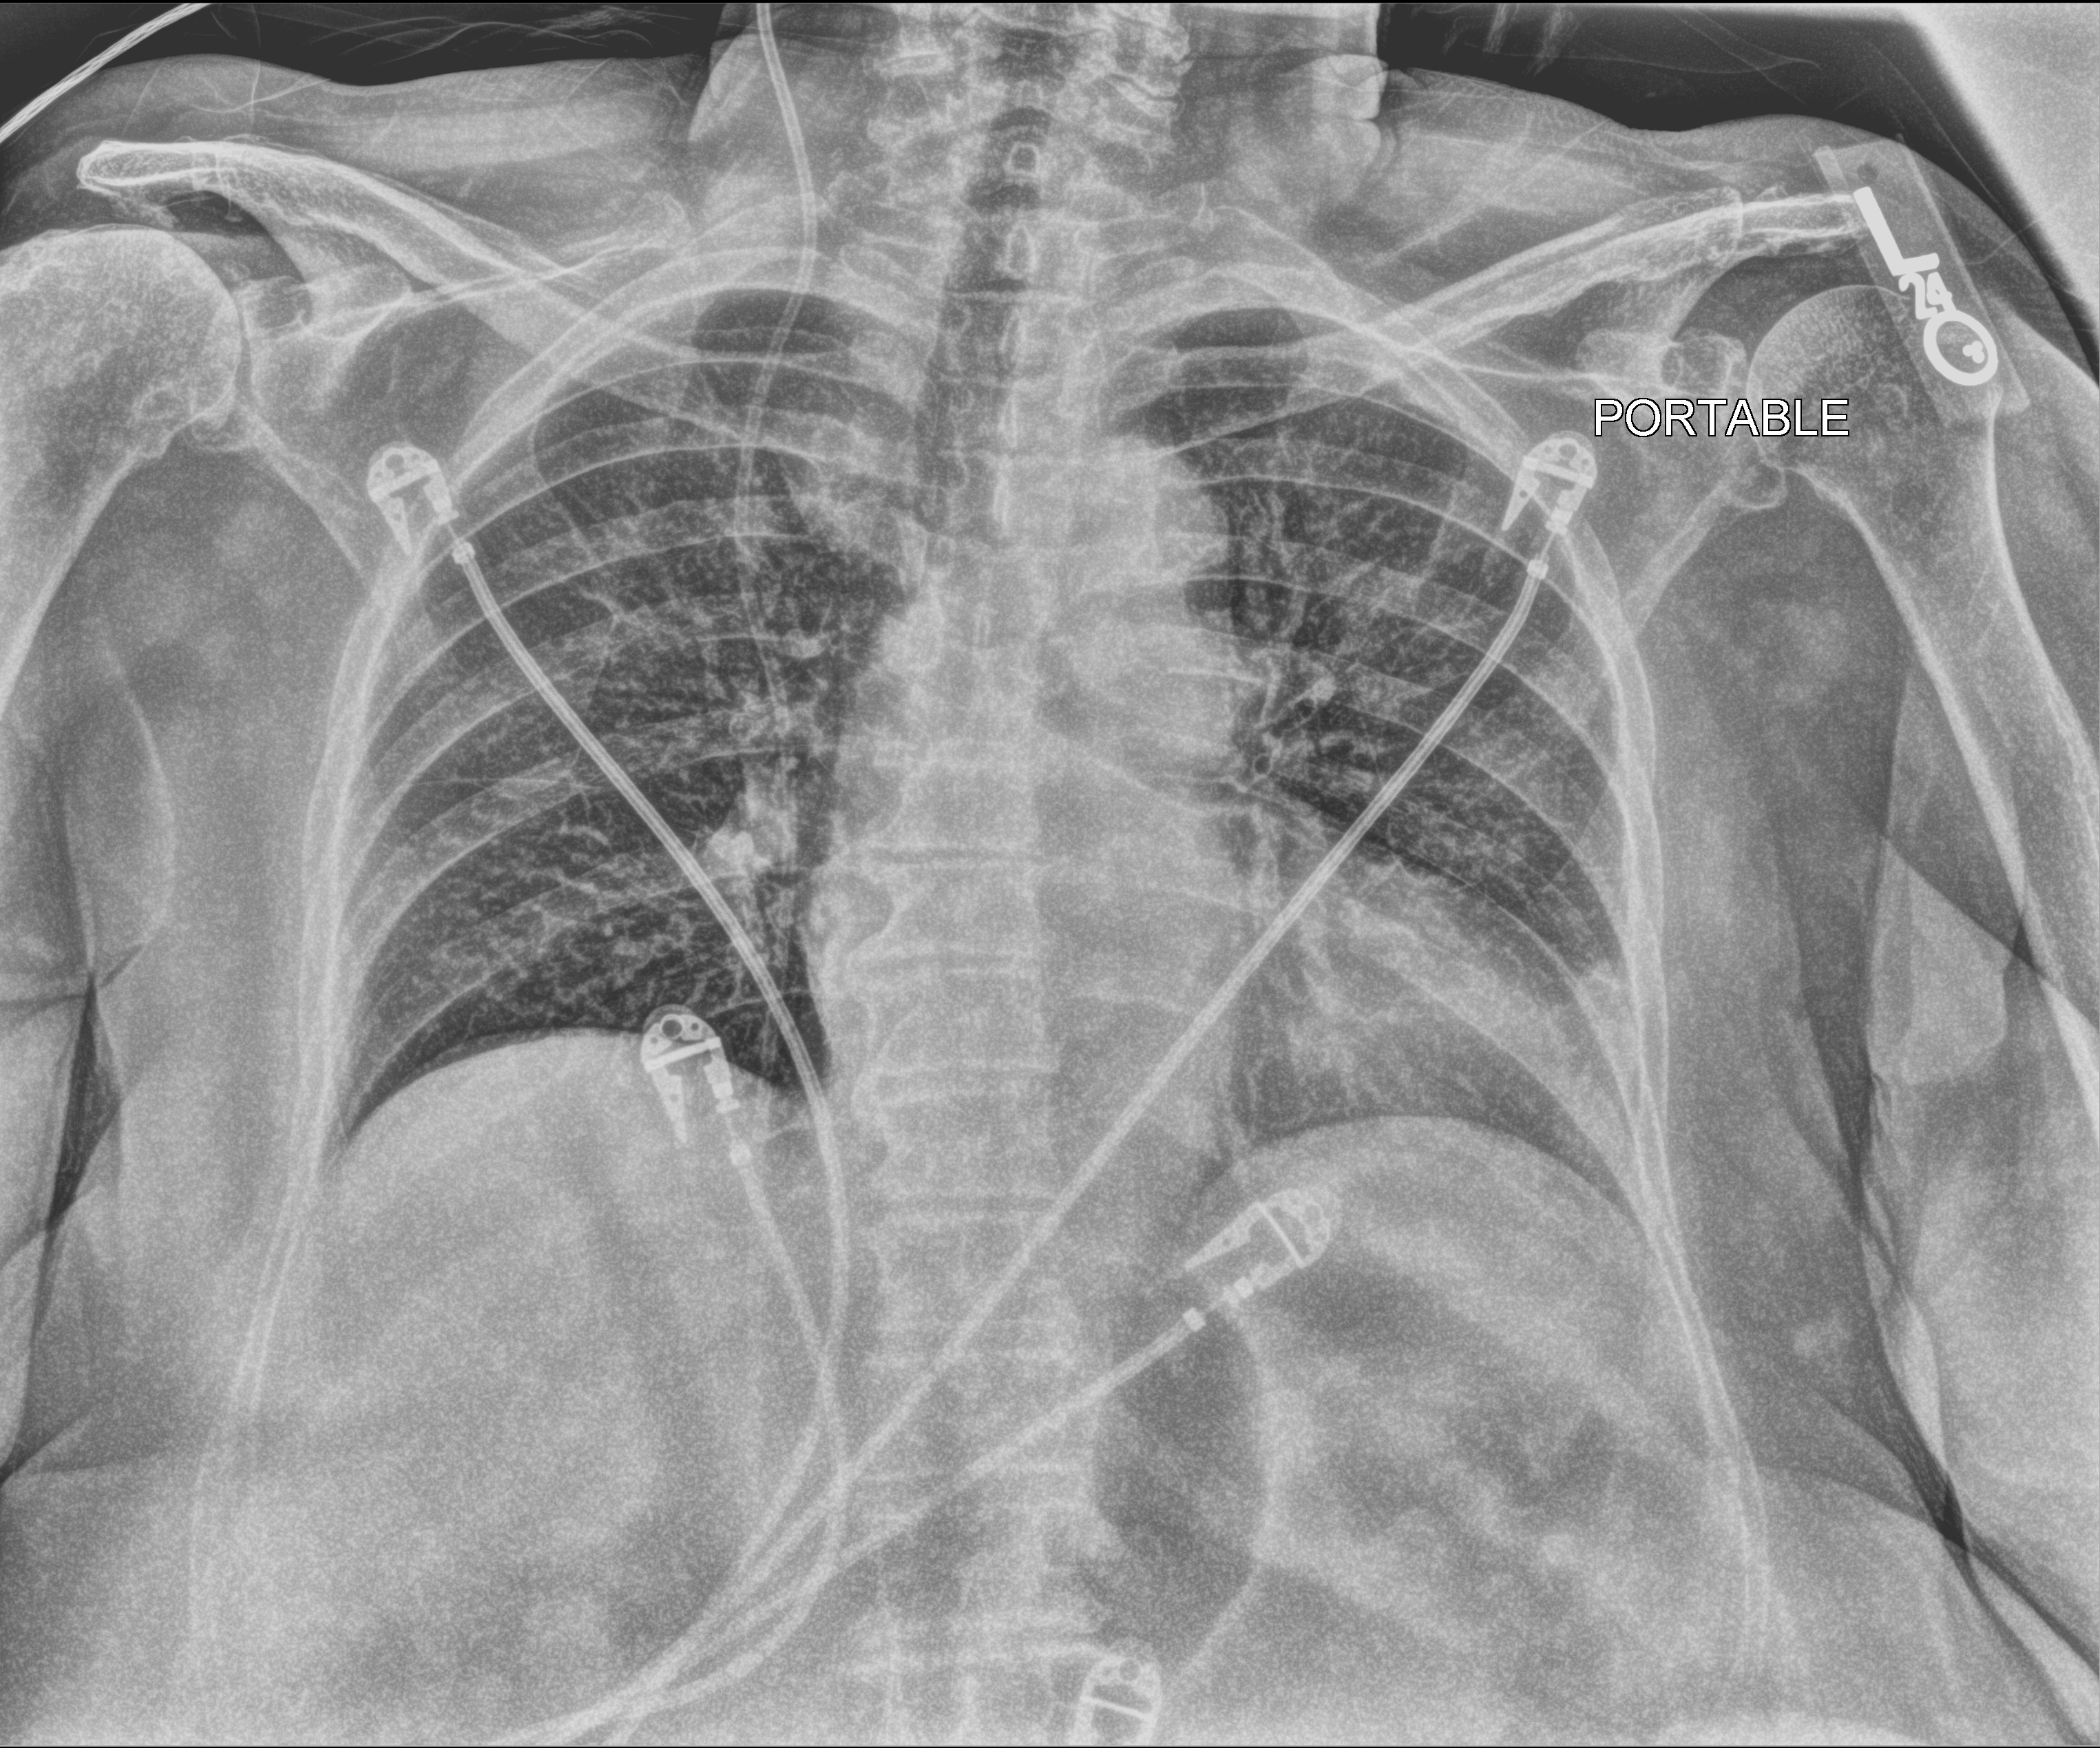
Portable chest radiograph; anteroposterior (AP) projection. Female patient hospitalised with COVID-19, age 75–90 years.
Admission-level facts for this patient (not findings on this image; timing relative to this image not recorded): diabetes (admission record): yes; mechanically ventilated during this hospital stay: yes; admitted to intensive care during this hospital stay: yes.